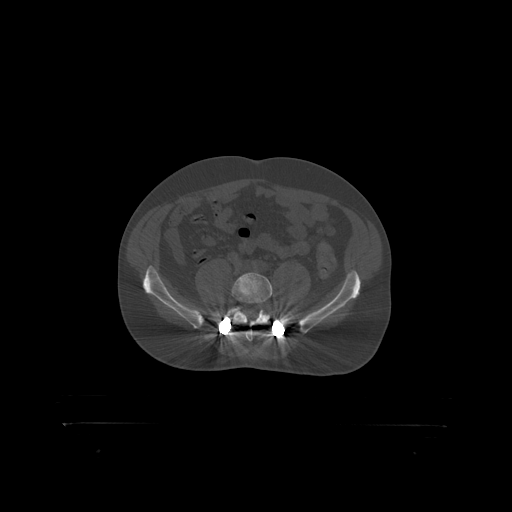
CT including the spine, one axial slice. Slice 200 of 399 in the series (ordered by position). 120 kVp. Bone window (W 1800 / L 400 HU). 1.25 mm slice thickness. 512 × 512 image matrix, field of view 650 × 650 mm. Male patient, age 46 years. From the clinical record (not read from this slice): primary cancer: skin.
Structures marked on this image (semi-automatically segmented with operator editing):
- L5 vertebra: bounding box <232,273,273,319> (left, top, right, bottom; pixels)